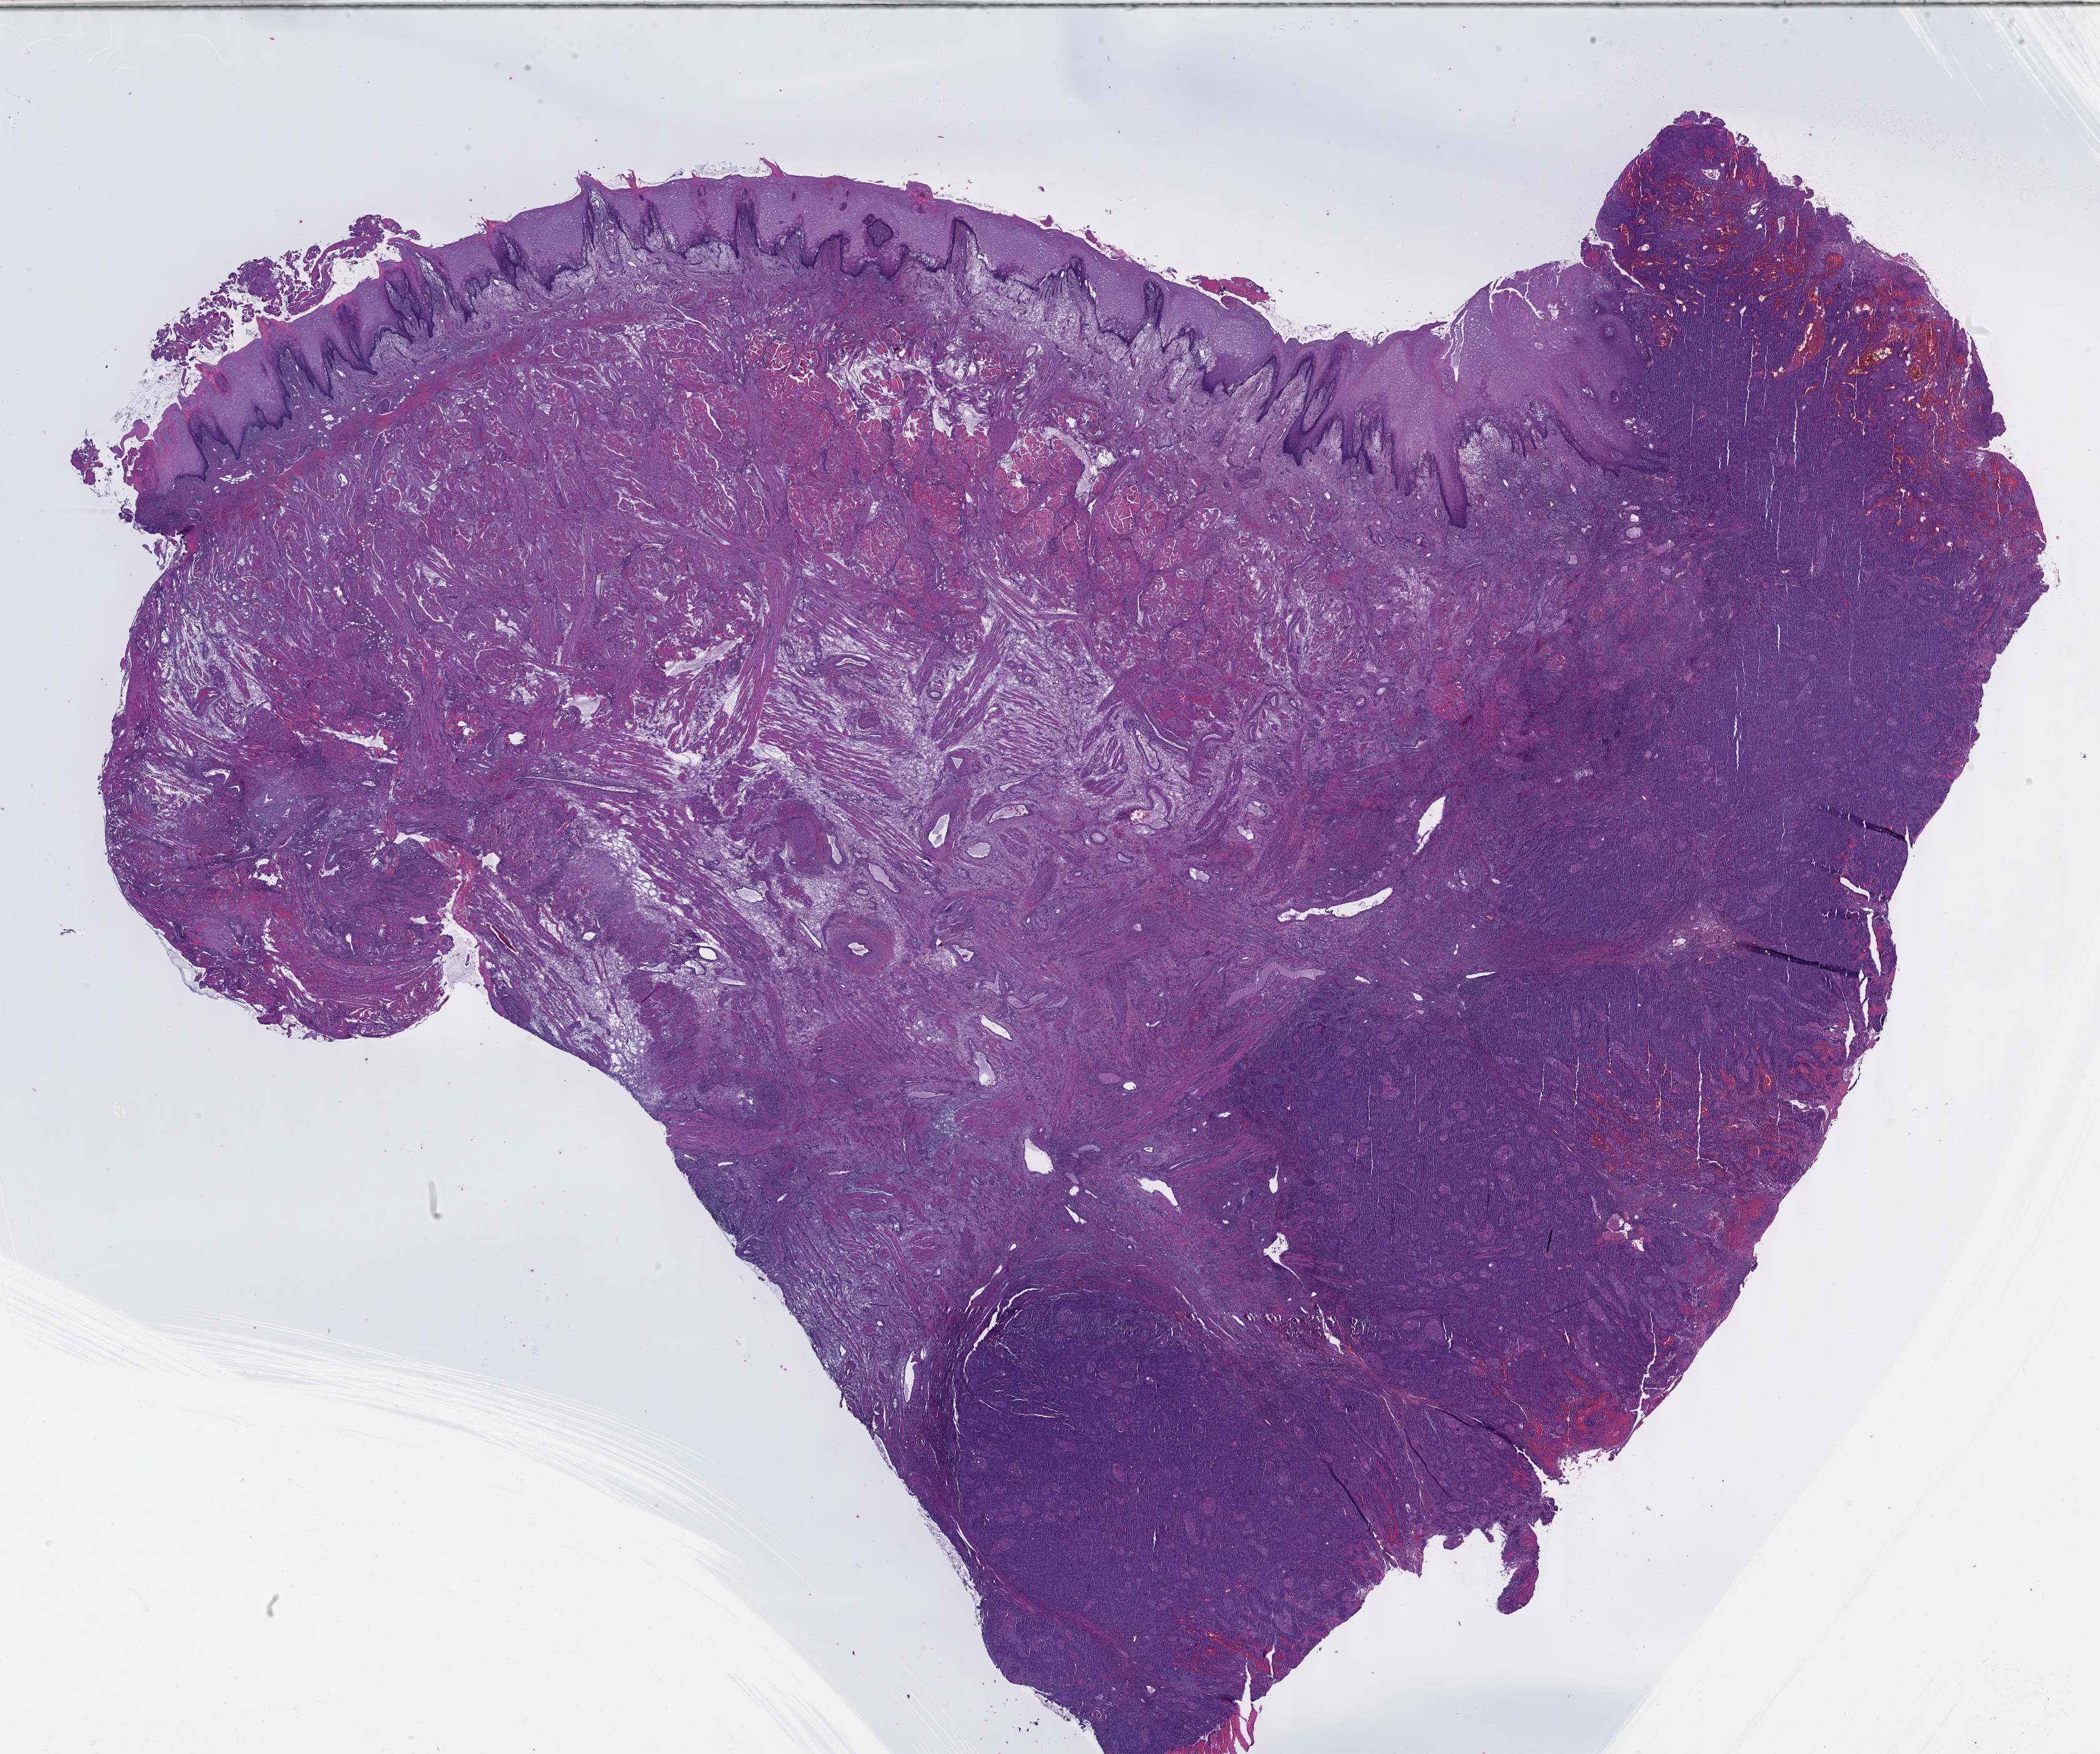
Digitized H&E-stained tissue section (whole slide), low-resolution overview of the scanned area, about 27.2 x 22.7 mm (slide scanned at 40x), formalin-fixed paraffin-embedded (FFPE) diagnostic section, head and neck, primary tumour sample. Male patient; age at initial diagnosis 50 years. Histologic grade: G2 (moderately differentiated).
Lymph nodes positive (case pathology): 2 of 50 examined. Histologic diagnosis: Squamous cell carcinoma, NOS. AJCC pathologic stage: IVA (7th edition). TNM: T4a N2b.